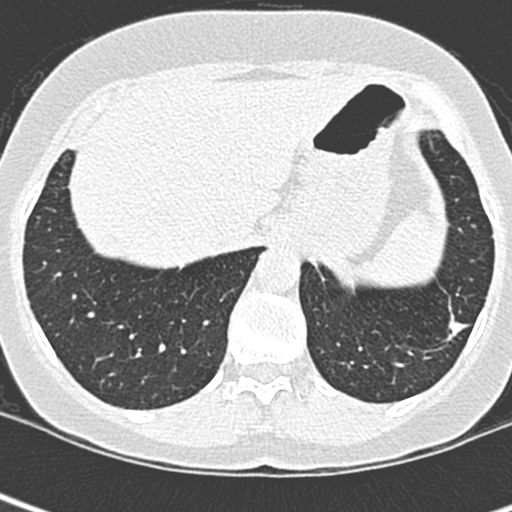
Low-dose screening chest CT, one axial slice; position 56 of 252 along the scan axis; 120 kVp; lung window (W 1500 / L -600 HU); 1.3 mm slice thickness; 512 × 512 image matrix, field of view 271 × 271 mm.
Structures marked on this image (outlined manually by an expert reader):
- lesion 1 (tumor, lower lobe of left lung): bounding box [x1, y1, x2, y2] px = [448, 316, 467, 335]